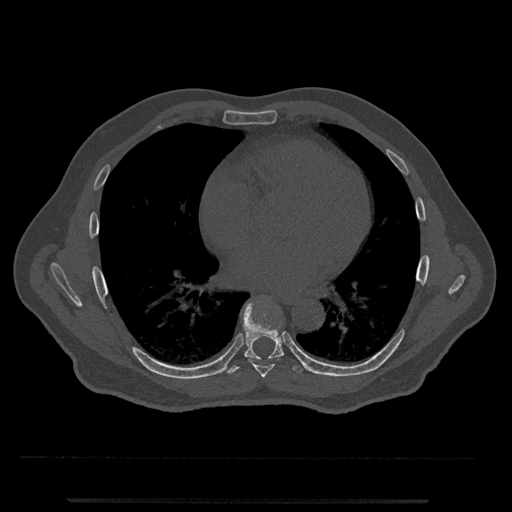
CT including the spine, one axial slice; reconstruction kernel Br40s/3; 120 kVp; bone window (W 1800 / L 400 HU); 0.5 mm slice thickness; 512 × 512 image matrix, field of view 419 × 419 mm. Patient: male, 63 years. Case-level facts recorded for this patient, not image findings: primary cancer: prostate.
Structures marked on this image (semi-automatic segmentation, software-assisted and operator-edited):
- T7 vertebra: bounding box (x1, y1, x2, y2) in pixels: (249, 356, 281, 379)
- T8 vertebra: (225, 298, 303, 375)